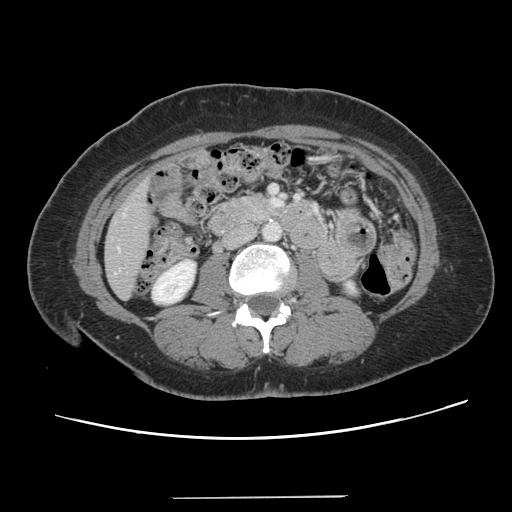
Contrast-enhanced abdominal CT, one axial slice. Position 33 of 141 along the scan axis. 120 kVp. Intravenous contrast given. Soft-tissue window (W 400 / L 40 HU). 2.5 mm slice thickness. 512 × 512 image matrix, field of view 366 × 366 mm. Female patient, age 53 years. Case-level facts recorded for this patient, not image findings: diagnosis: colorectal cancer liver metastases, imaged before liver resection; multiple liver metastases: no; largest metastasis: 14.5 cm; chemotherapy before resection: yes.
Annotated regions visible in this slice (outlined manually by an expert reader):
- liver: bounding box [x1, y1, x2, y2] px = [106, 185, 151, 299]
- planned liver remnant (the part of the liver to remain after resection): [106, 209, 150, 298]